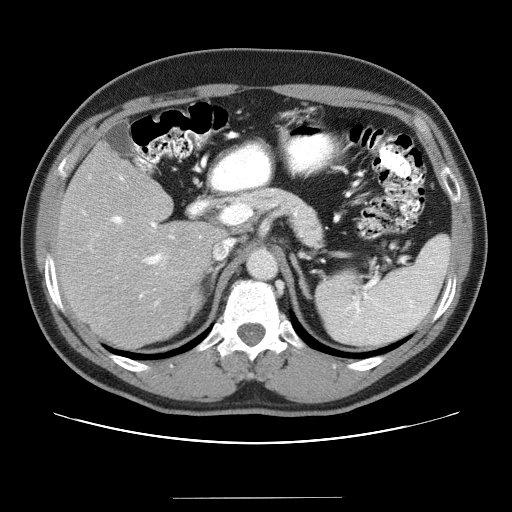
Contrast-enhanced abdominal CT (liver protocol), one axial slice. Slice 19 of 40 in the series (ordered by position). 120 kVp. Soft-tissue window (W 400 / L 40 HU). 5 mm slice thickness. 512 × 512 image matrix. Case-level facts recorded for this patient, not image findings: diagnosis: hepatocellular carcinoma (patient treated with transarterial chemoembolisation; whether this scan precedes or follows treatment is not stated here); TNM stage (as recorded): Stage-IVA; Child-Pugh class: B; tumour nodularity: multinodular.
Annotated regions visible in this slice (semi-automatic segmentation, software-assisted and operator-edited):
- liver parenchyma outside the tumour (the mass and vessels are separate outlines, so this box may not span the whole liver): bounding box (x1, y1, x2, y2) in pixels: (56, 142, 226, 348)
- liver vessels: (83, 175, 201, 306)